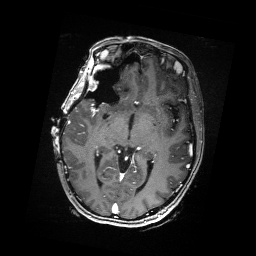
Brain MRI from a brain-tumour surgery series, one axial slice. Slice 98 of 176 in the series (ordered by position). T1-weighted post-contrast. 1 mm slice thickness. 256 × 256 image matrix, field of view 256 × 256 mm. From the clinical record (not read from this slice): histopathology: Metastatic Carcinoma from Breast primary; tumour location: Right Frontal.
Annotated regions visible in this slice (outlined manually by an expert reader):
- residual tumour: bounding box (x1, y1, x2, y2) in pixels: (105, 70, 115, 88)